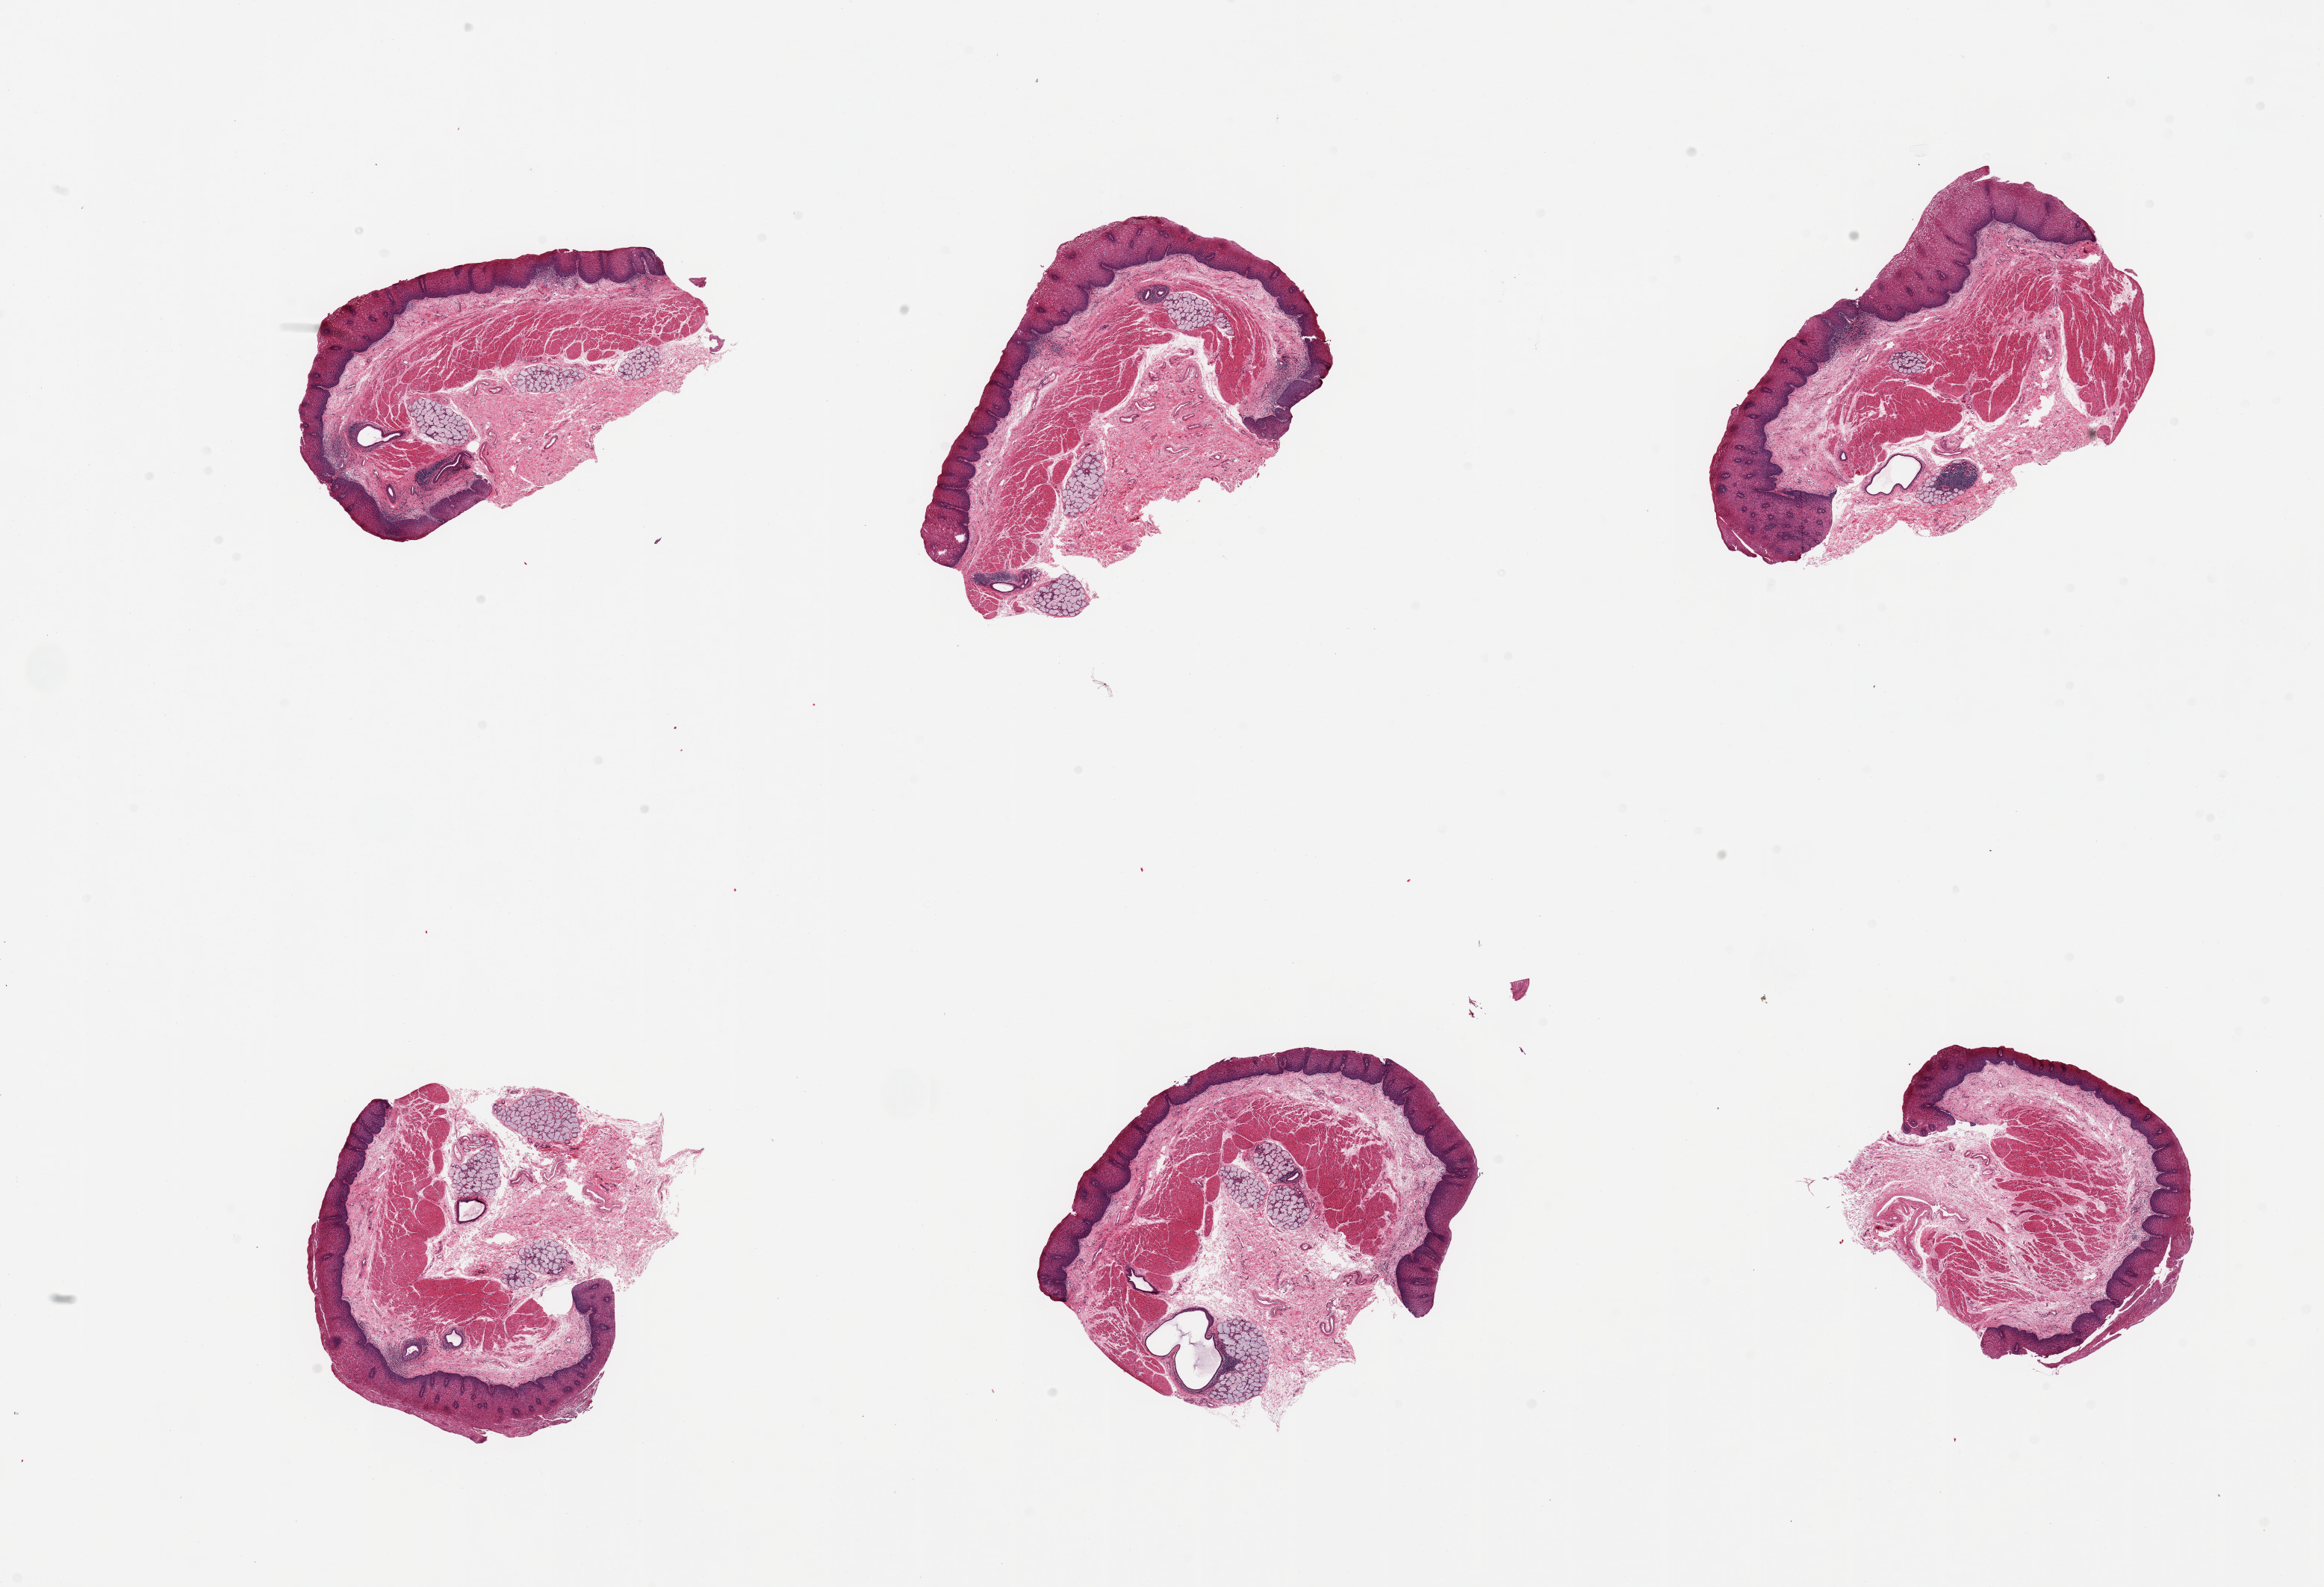
Whole-slide image, hematoxylin and eosin (H&E) stain, brightfield — shown as a low-resolution overview of the whole scanned area (about 24.6 x 16.8 mm, acquisition: 20x scan), PAXgene-fixed paraffin-embedded (PFPE) section, target tissue: esophageal mucous membrane, tissue donor sample. Donor sex: male.
- pathologist's review note for this sample: 6 pieces; prominent submucosal glands; thick submucosa up to 2 mm thick